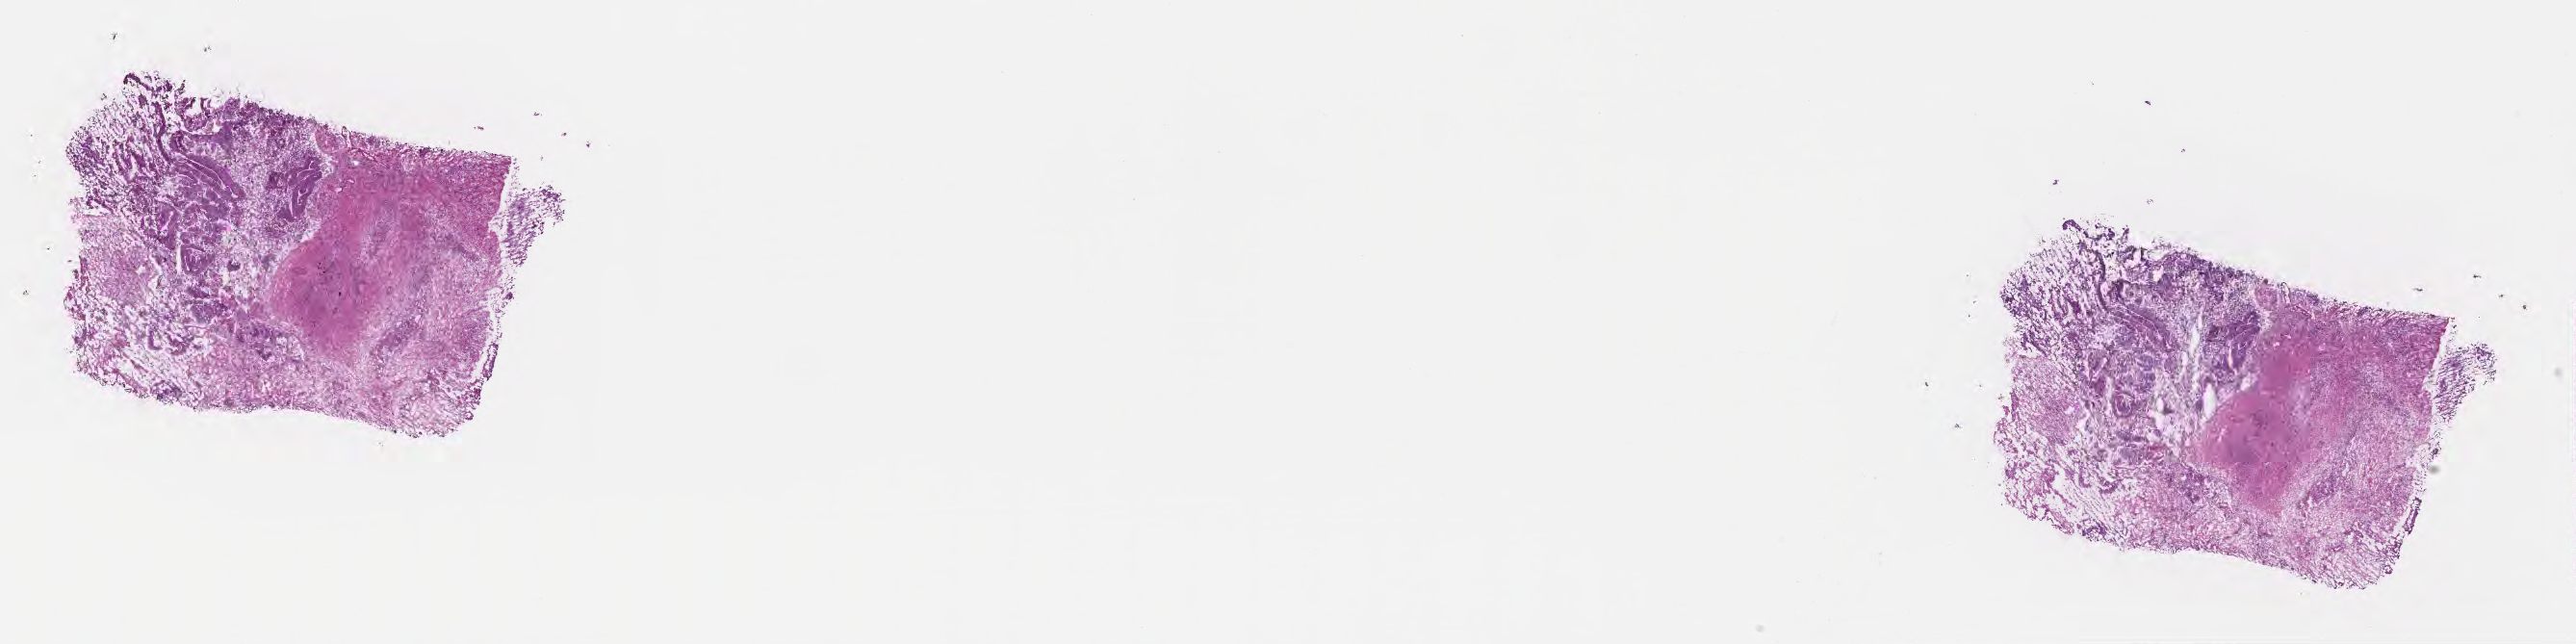
Digitized hematoxylin and eosin (H&E)-stained section, shown as a low-resolution overview of the whole scanned area (about 21.6 x 5.4 mm). Frozen section (tissue freezing medium). Primary tumor. Anatomic site: sigmoid colon. Male patient; age at initial diagnosis 82 years. Tumor grade: G2 (moderately differentiated). Slide review estimates, as recorded: tumor cells 80%, tumor nuclei 65%, stromal cells 0%, necrosis 0%, normal cells 20%. Infiltration values recorded for this section: lymphocyte infiltration 0%, monocyte infiltration 0%, neutrophil infiltration 0%.
- AJCC pathologic stage: Stage IIA
- diagnosis: Adenocarcinoma, NOS